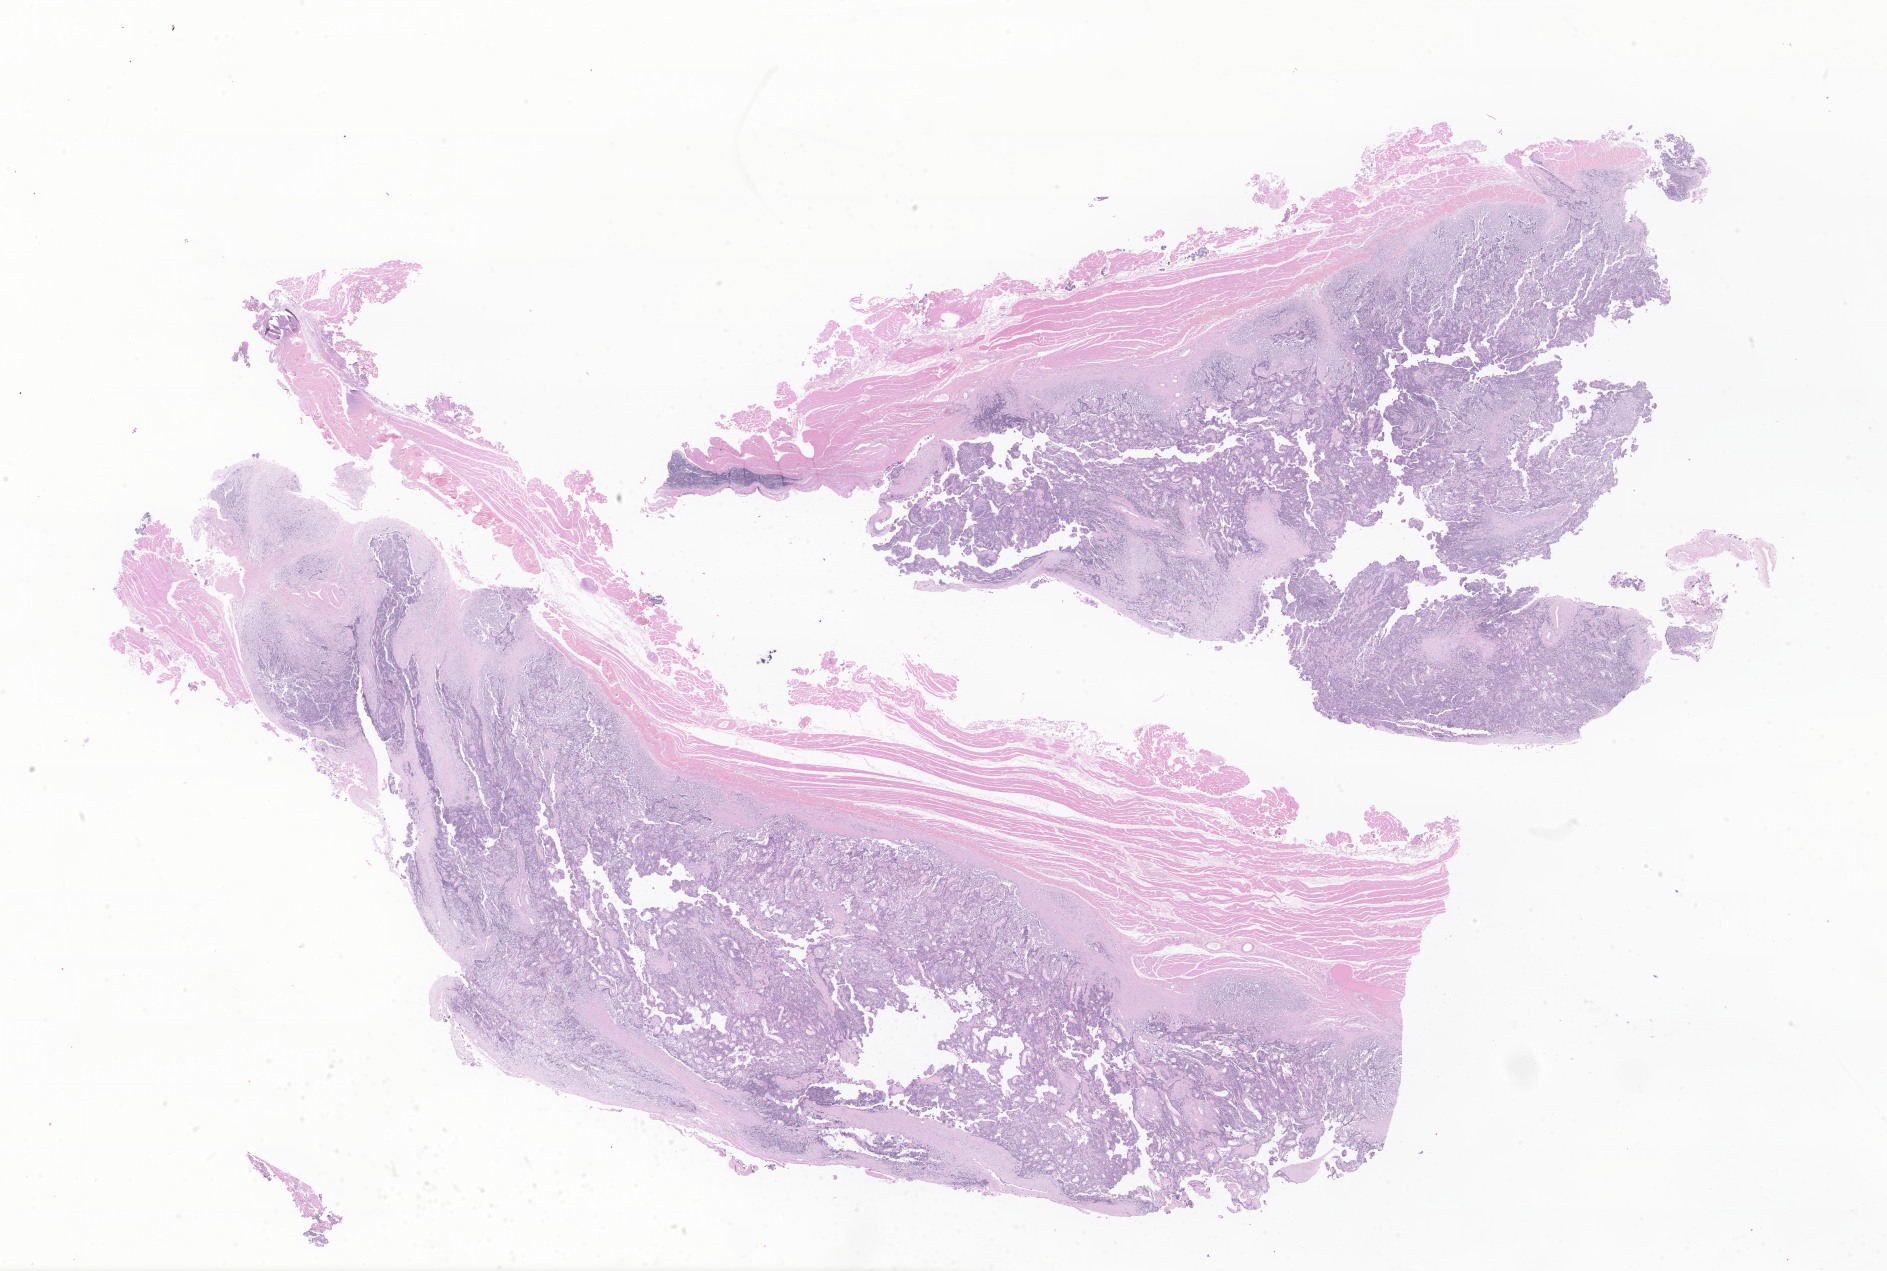
Whole-slide image, hematoxylin and eosin (H&E) stain of tumor tissue from the soft tissues of head and neck, low-resolution overview of the scanned area, about 31.8 x 21.4 mm; formalin-fixed, paraffin-embedded (FFPE) tissue. Patient: male, age 79 months (6 years 7 months).
Tissue or organ of origin (case record): connective, subcutaneous and other soft tissues of head, face, and neck. Diagnosis (ICD-O-3 morphology term): Alveolar rhabdomyosarcoma.